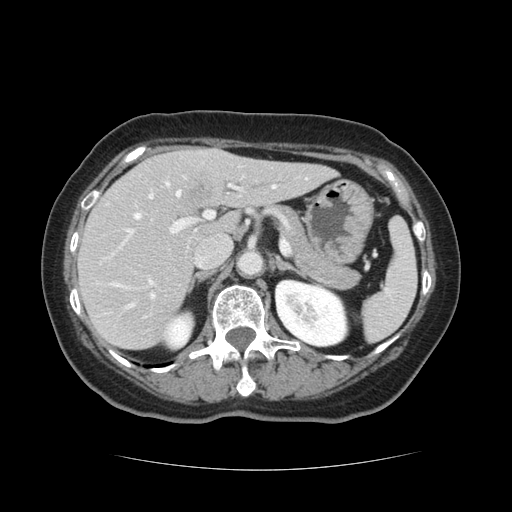
Contrast-enhanced abdominal CT, one axial slice. Slice 74 of 128 in the series (ordered by position). 120 kVp. Intravenous contrast given. Soft-tissue window (W 400 / L 40 HU). 512 × 512 image matrix, field of view 366 × 366 mm. Female patient, age 67 years. Case-level facts recorded for this patient, not image findings: diagnosis: colorectal cancer liver metastases, imaged before liver resection; multiple liver metastases: yes; largest metastasis: 3 cm; disease in both lobes: yes.
Annotated regions visible in this slice (manually delineated by an expert):
- hepatic veins: bounding box <113,183,276,307> (left, top, right, bottom; pixels)
- liver: <78,147,329,349>
- planned liver remnant (the part of the liver to remain after resection): <78,159,329,349>
- portal vein (with intrahepatic branches): <122,175,242,299>
- liver metastasis: <193,184,208,196>